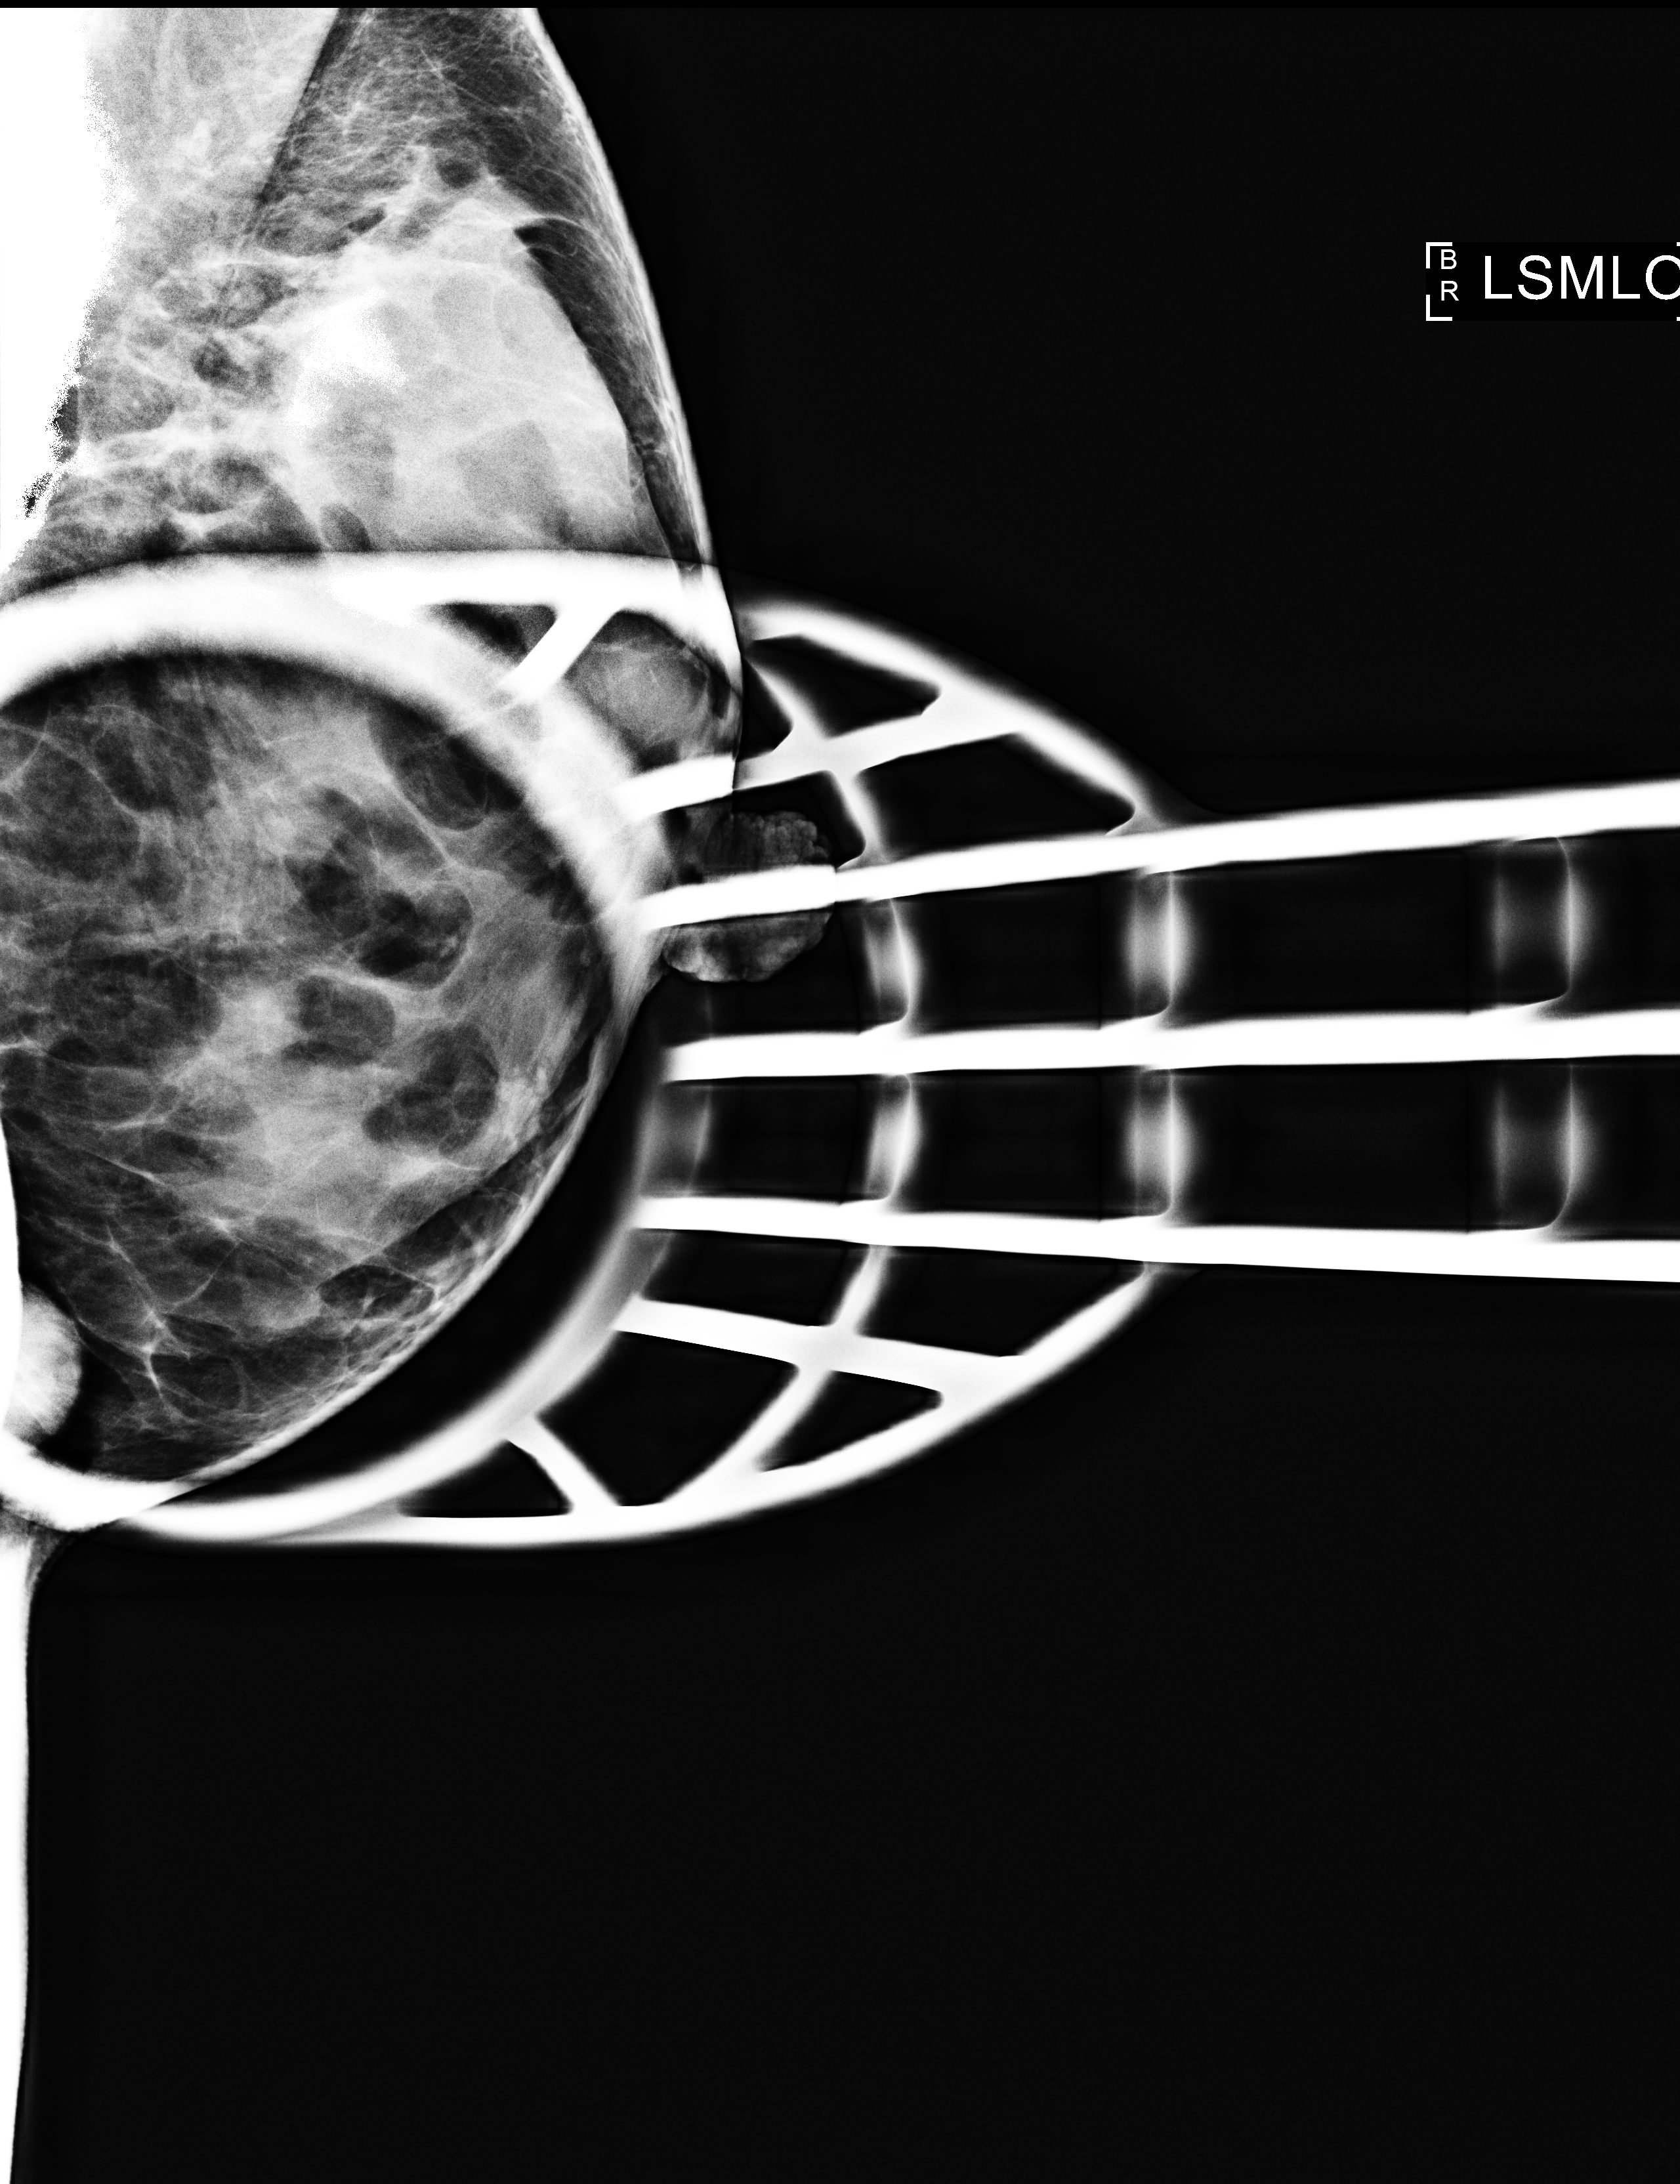
Digital mammogram (FFDM); left breast; mediolateral oblique (MLO) view (spot compression); additional work-up view. Patient aged 42 years (female).
Final BI-RADS assessment for this screening round (tomosynthesis exam, both breasts): category 2.